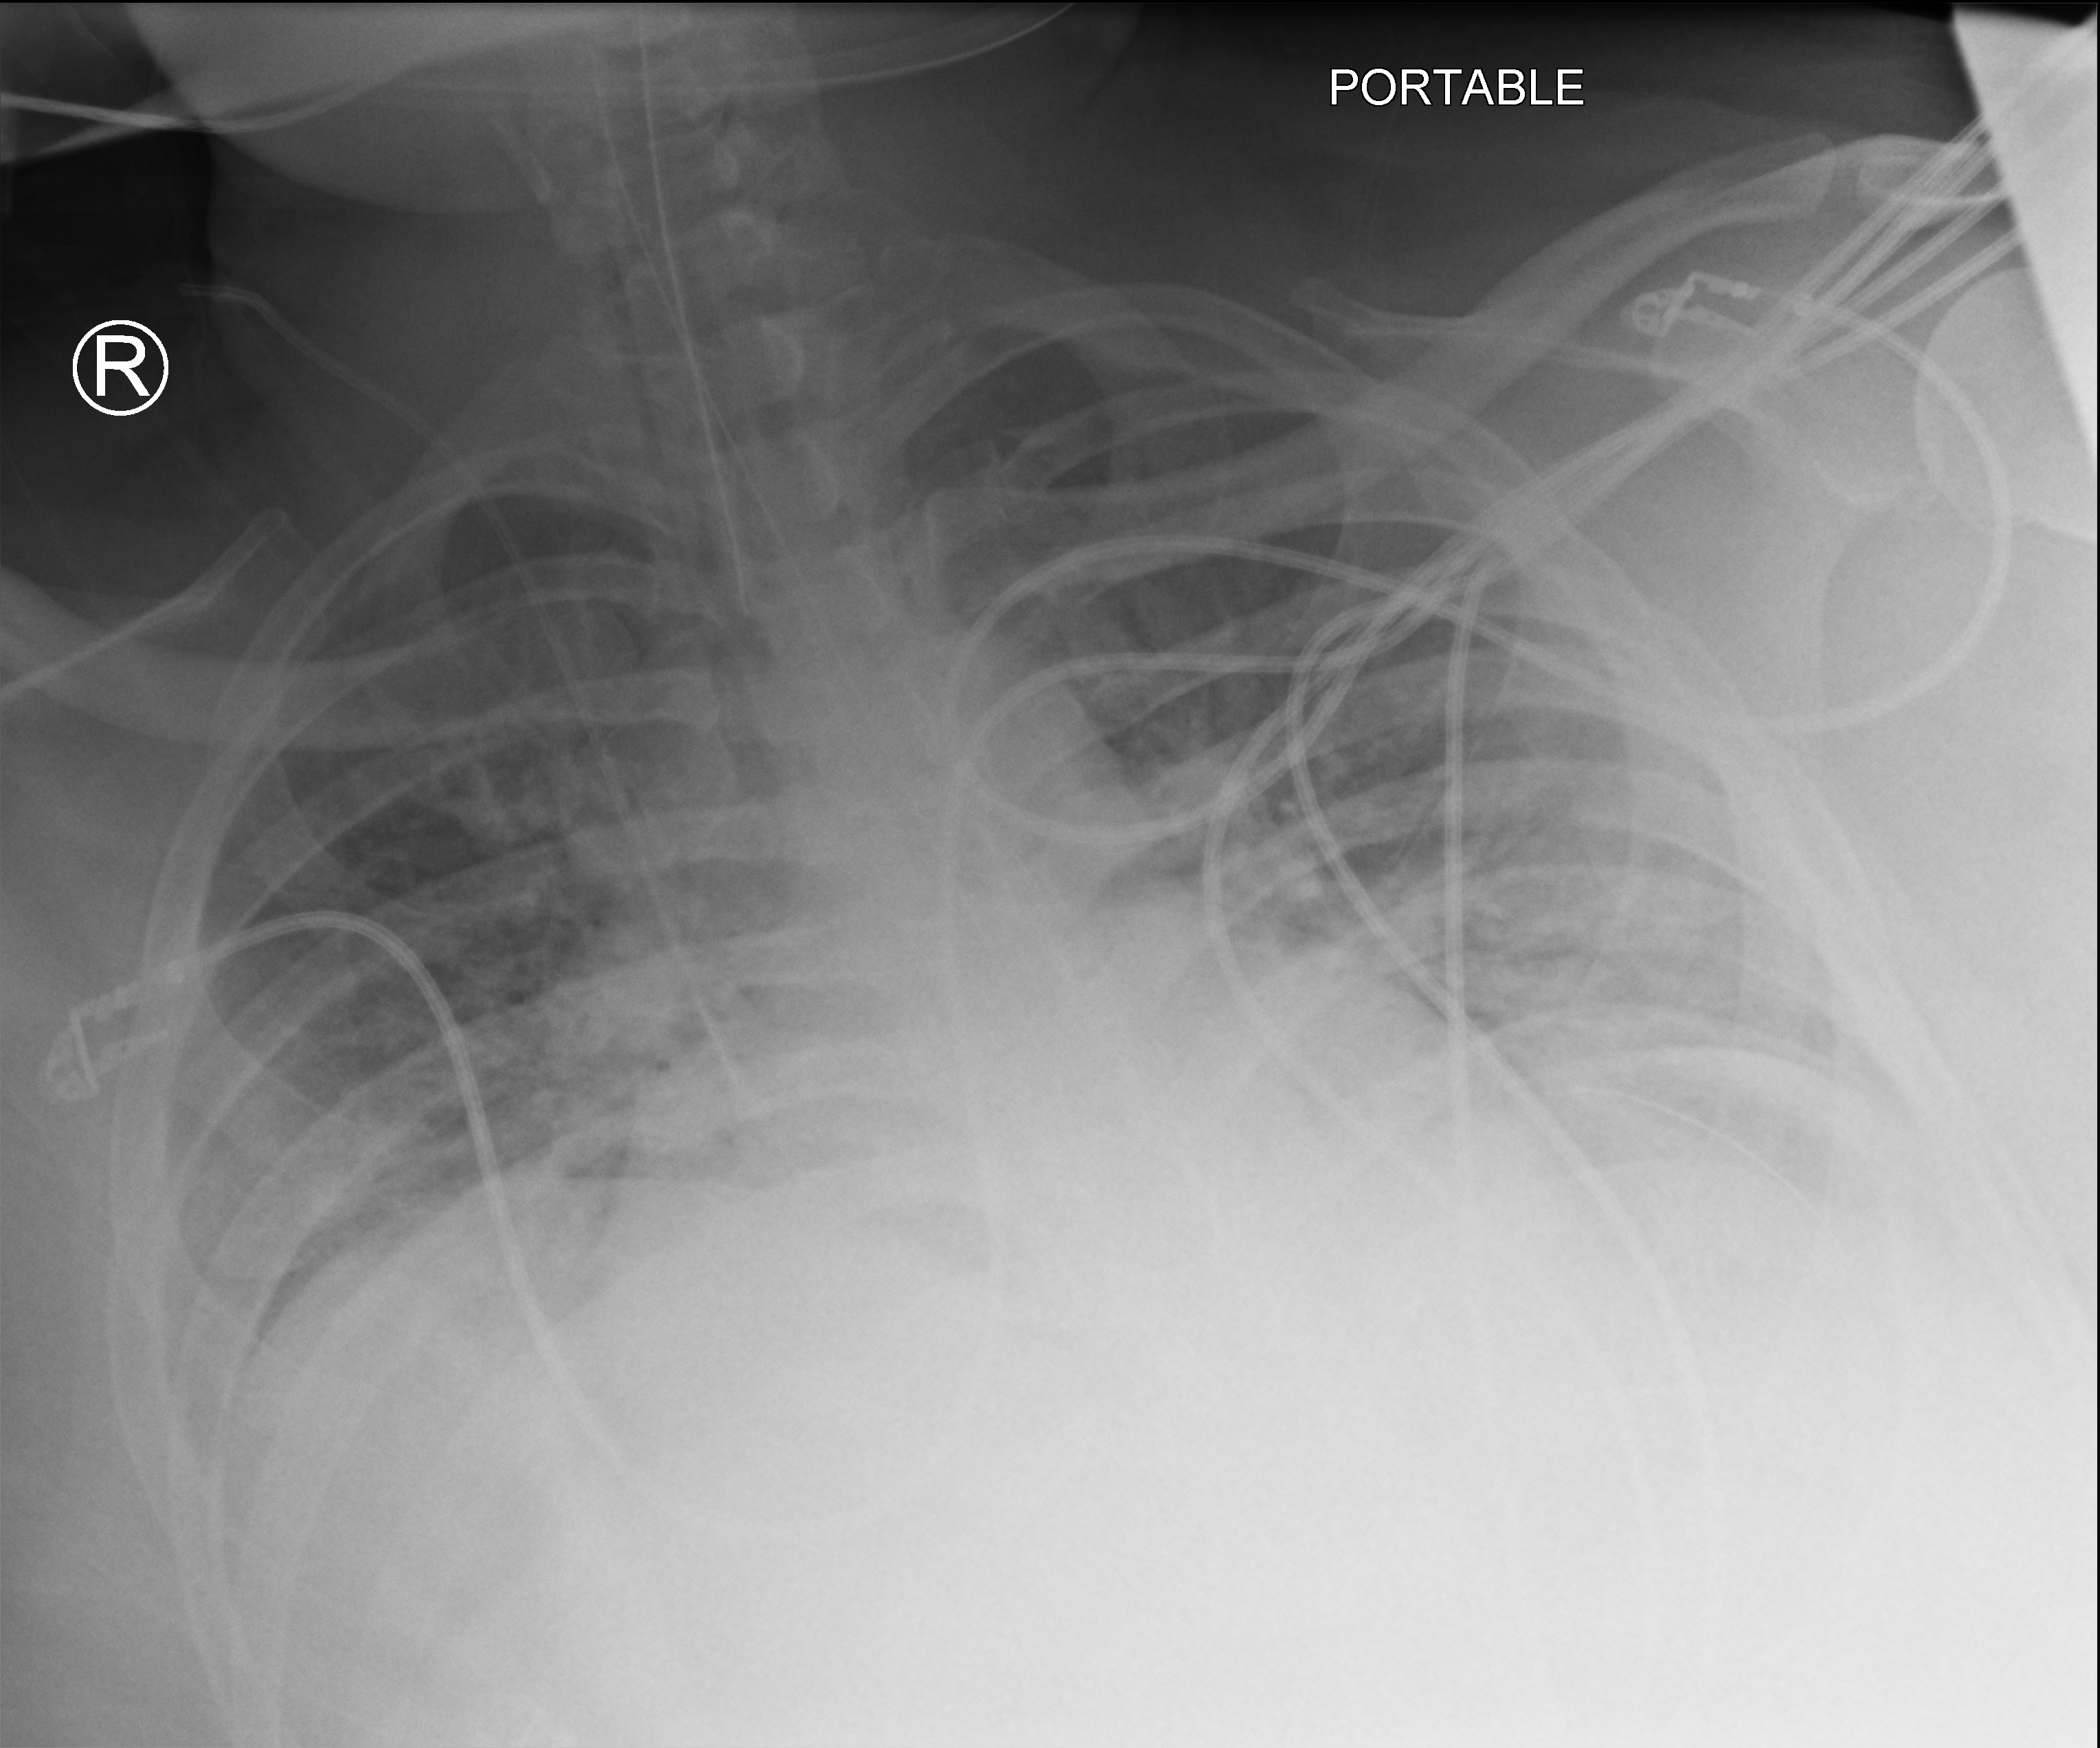
Bedside chest radiograph (computed radiography); anteroposterior (AP) projection. Patient hospitalised with COVID-19; male, aged 18–59 years.
Admission-level facts for this patient (not findings on this image; timing relative to this image not recorded):
- COPD (admission record): yes
- admitted to intensive care during this hospital stay: yes
- length of hospital stay: 69 days